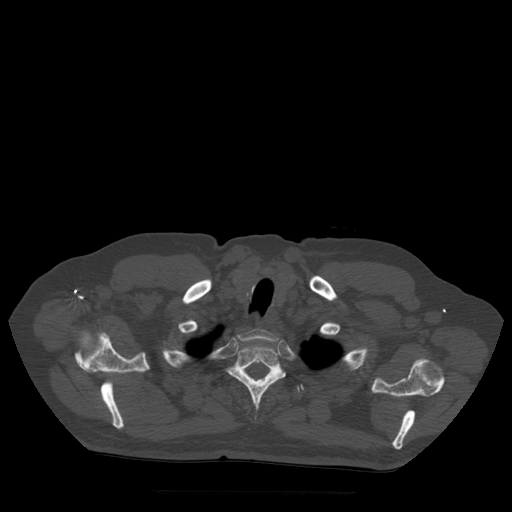
CT including the spine, one axial slice; position 425 of 522 along the scan axis; bone window (W 1800 / L 400 HU); 1.25 mm slice thickness; 512 × 512 image matrix, field of view 420 × 420 mm. Patient age 72 years. Case-level facts recorded for this patient, not image findings: primary cancer: prostate.
Outlined on this slice (semi-automatic segmentation, software-assisted and operator-edited):
- T1 vertebra: box from (x=238, y=329) to (x=278, y=342) px
- T2 vertebra: (x=228, y=344)–(x=286, y=409)
- T3 vertebra: (x=247, y=374)–(x=300, y=393)